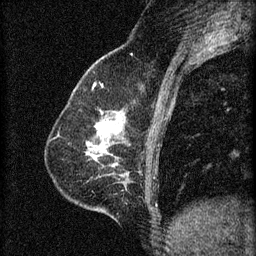
Breast MRI (dynamic contrast-enhanced), one sagittal slice; slice 23 of 60 in the series (ordered by position); 3 images stored at this slice position (order not interpretable as contrast timing); 1.5 T; TE 4.2 ms, TR 8.2 ms; 2 mm slice thickness; 256 × 256 image matrix, field of view 180 × 180 mm. Female patient, age 59 years.
Structures marked on this image (semi-automatic segmentation, software-assisted and operator-edited):
- analysis volume of interest (the breast-tissue region the enhancement analysis was run in; not a lesion): bounding box (x1, y1, x2, y2) in pixels: (63, 104, 132, 161)
- tumour enhancement mask (voxels above the 70 % enhancement threshold inside the analysis volume of interest): (97, 122, 114, 137)